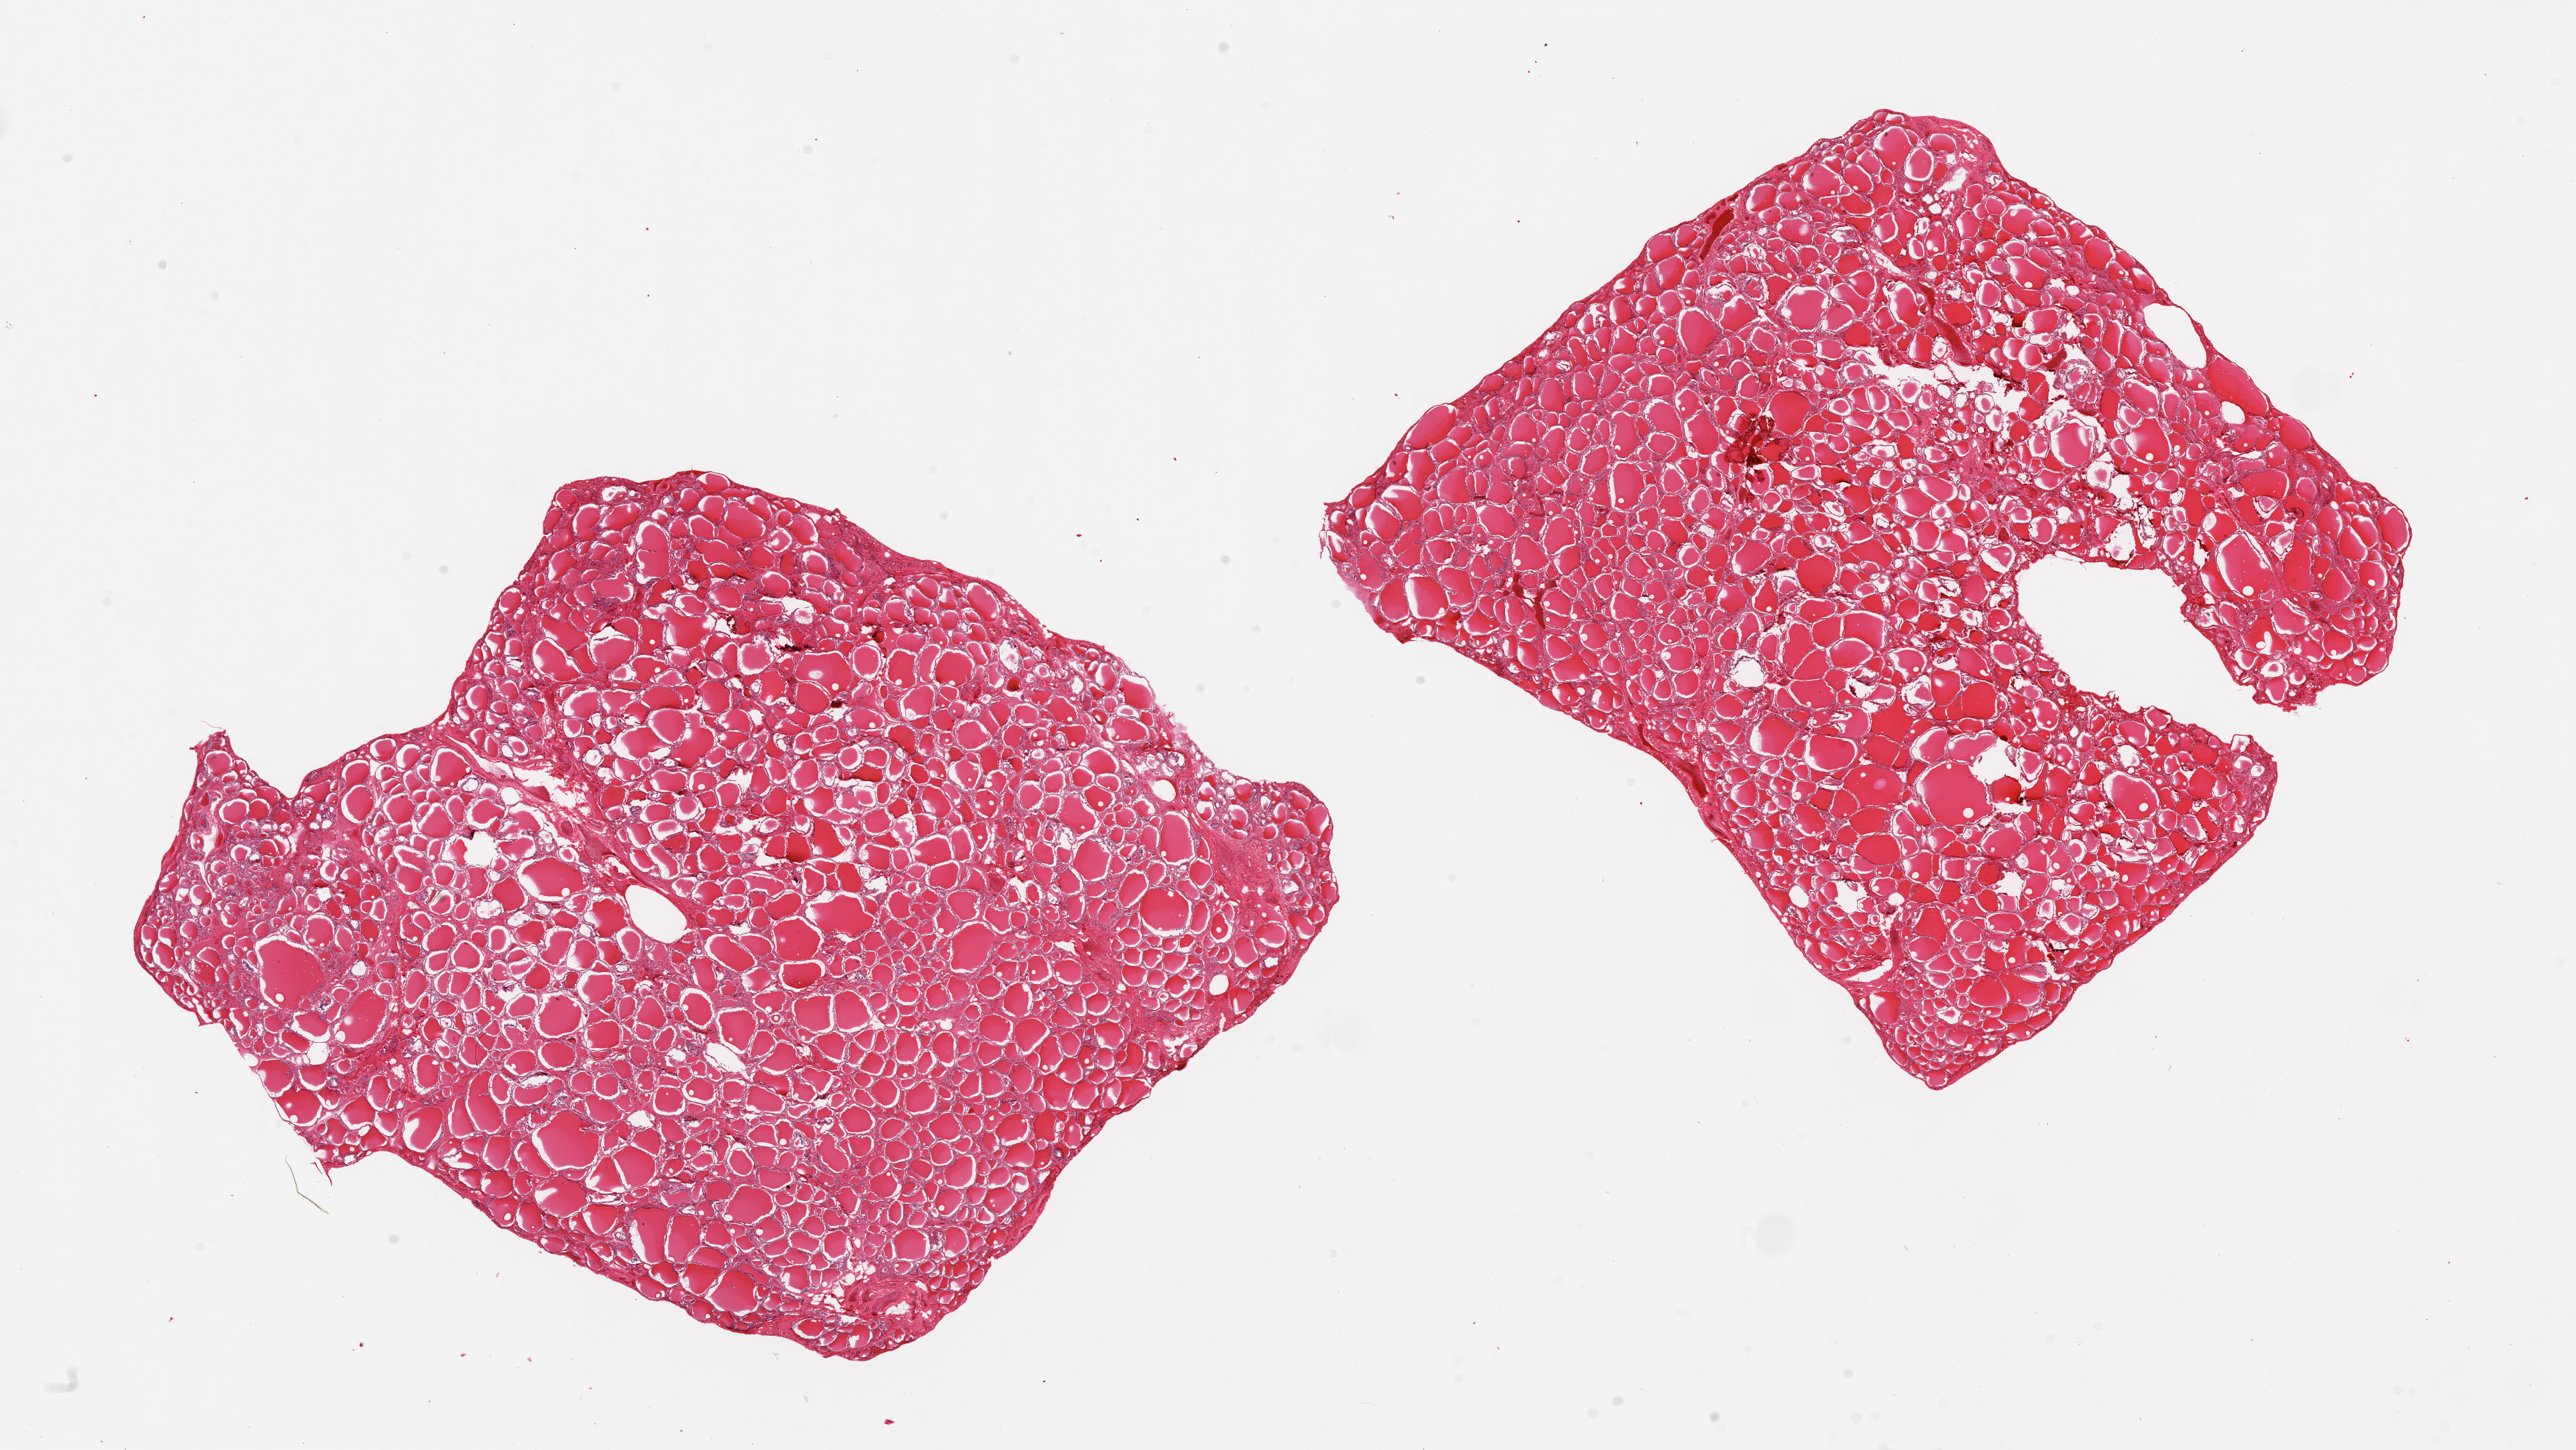
Whole-slide image, H&E stain, brightfield, a low-resolution overview of the entire scanned area, about 30.5 x 17.2 mm (slide scanned at 20x); PAXgene-fixed paraffin-embedded (PFPE) section; target tissue: thyroid; donor tissue sample.
- reviewer comment on this tissue sample: 2 pieces, no significant abnormalities